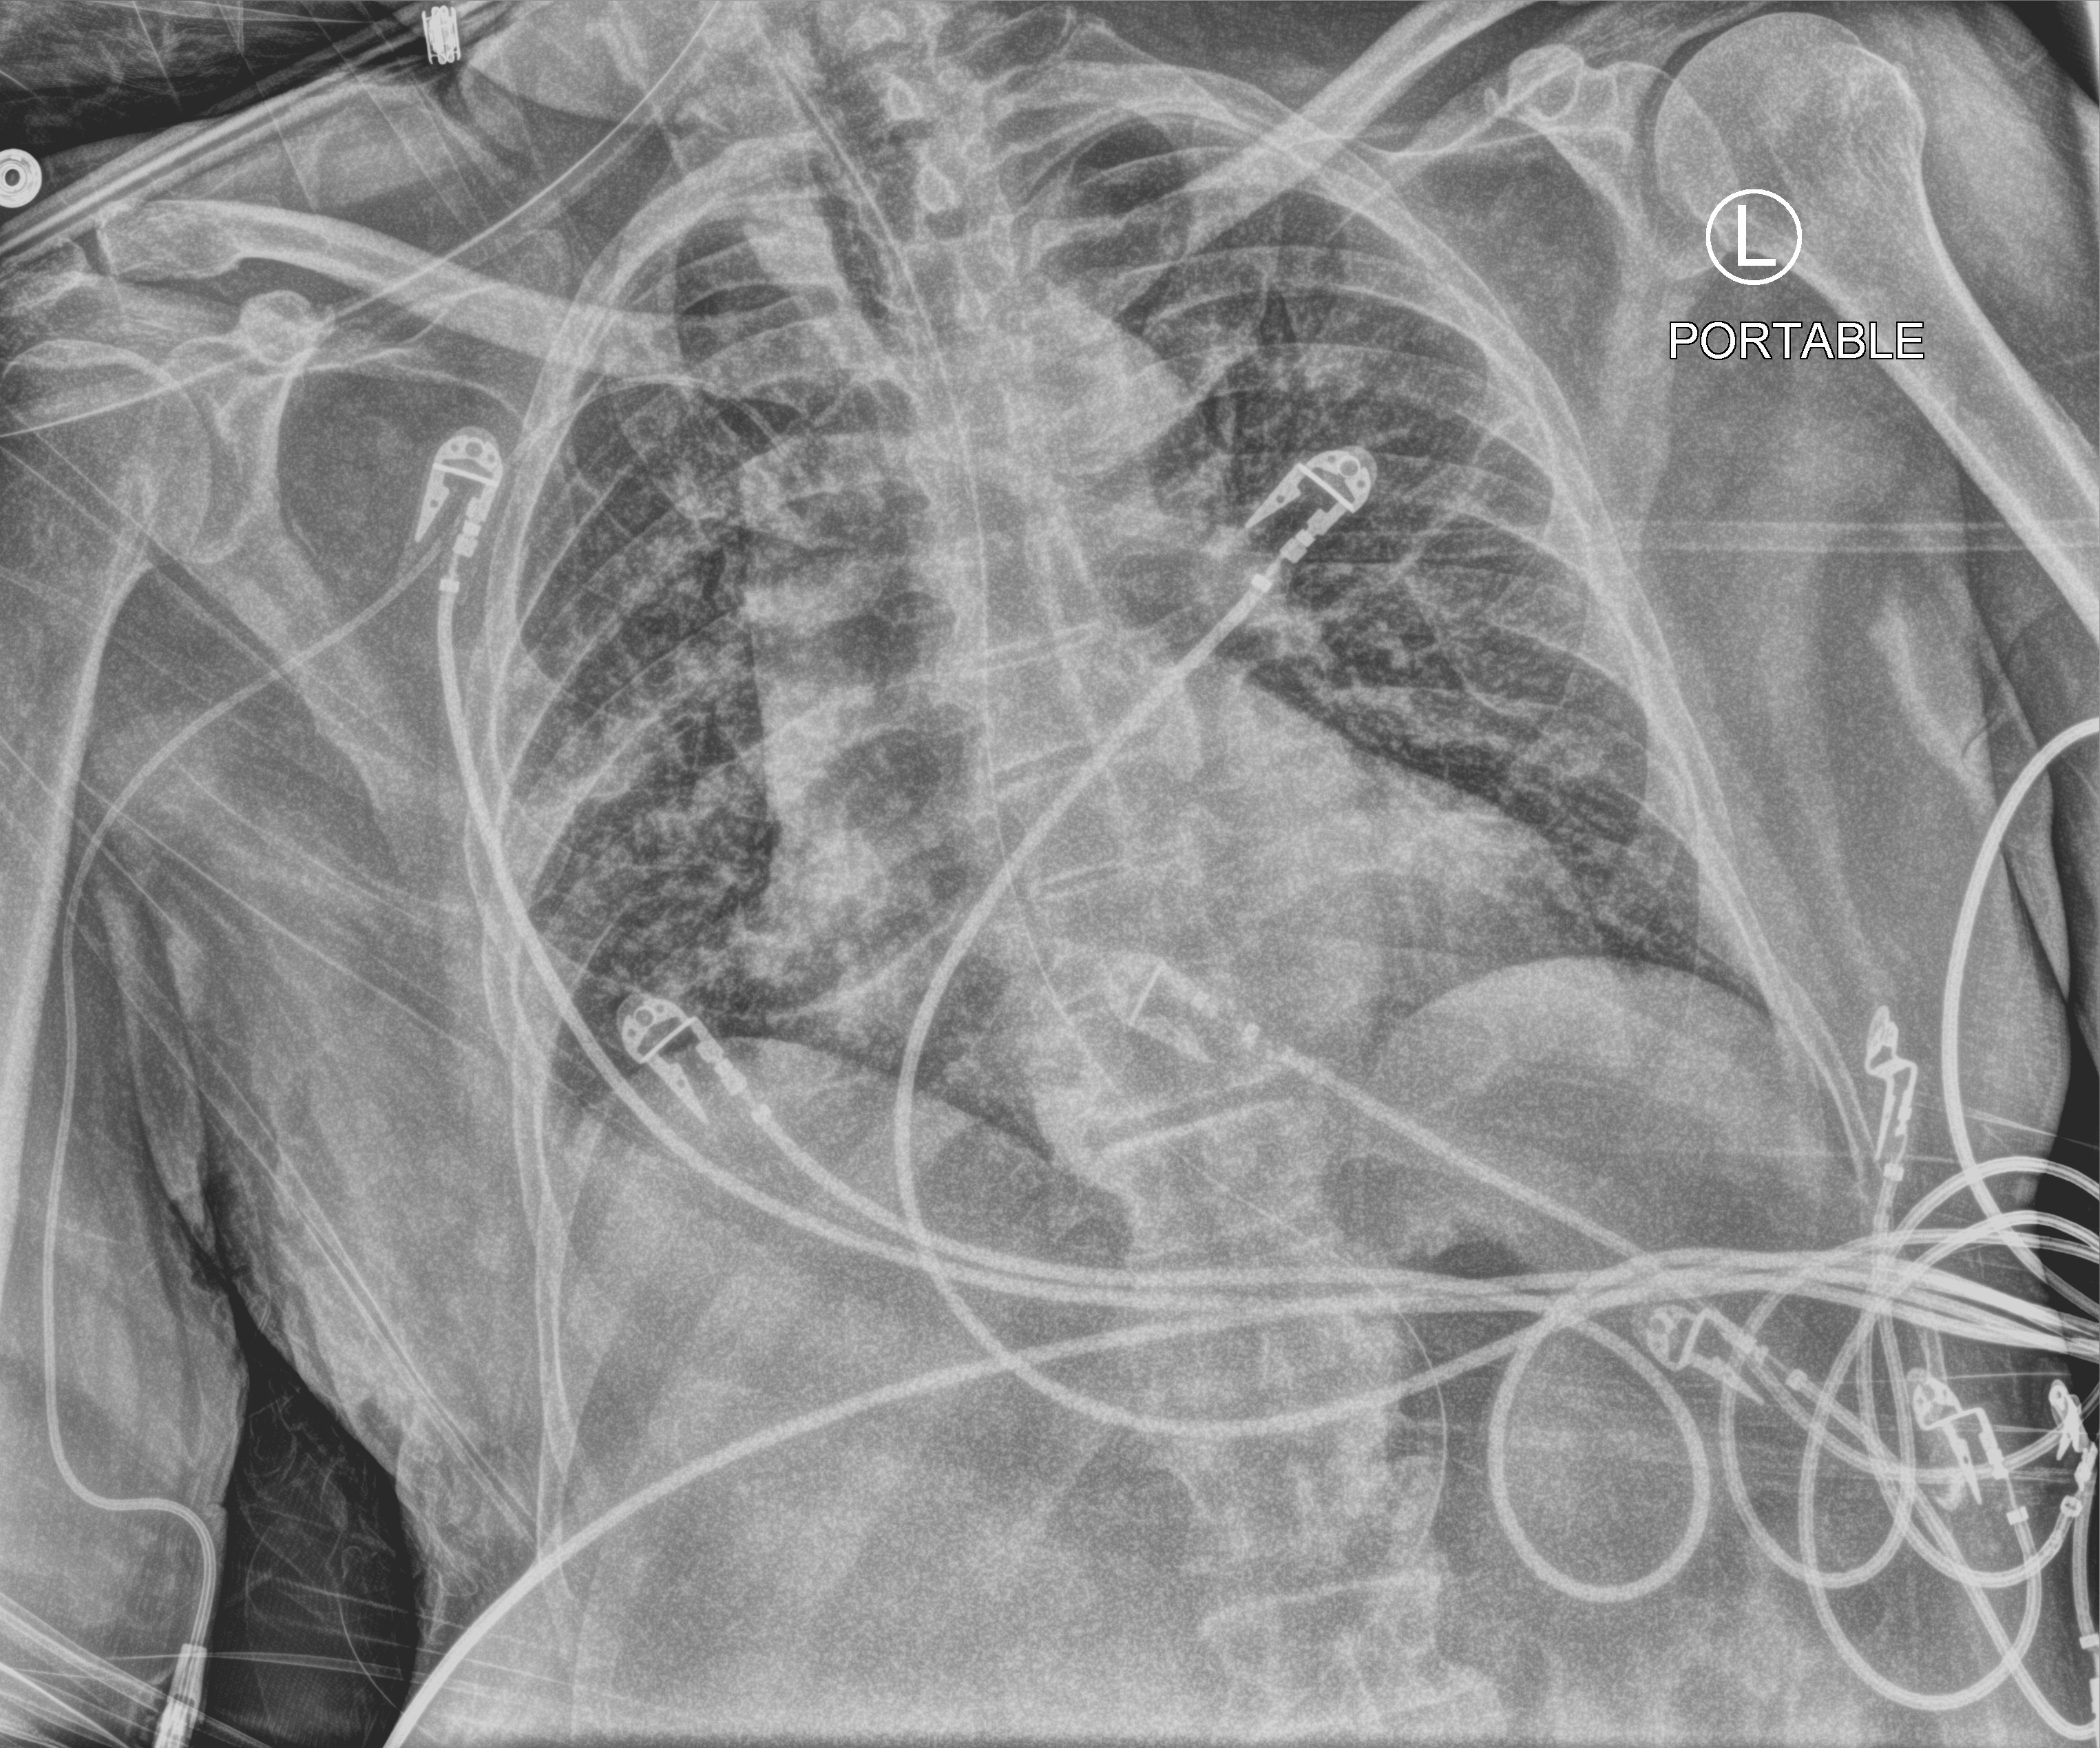
Bedside chest radiograph (computed radiography). Male patient hospitalised with COVID-19, age 60–74 years.
Hospital-stay facts (about this admission, not read from this image; timing relative to this image not recorded): mechanically ventilated during this hospital stay: yes; length of hospital stay: 31 days.